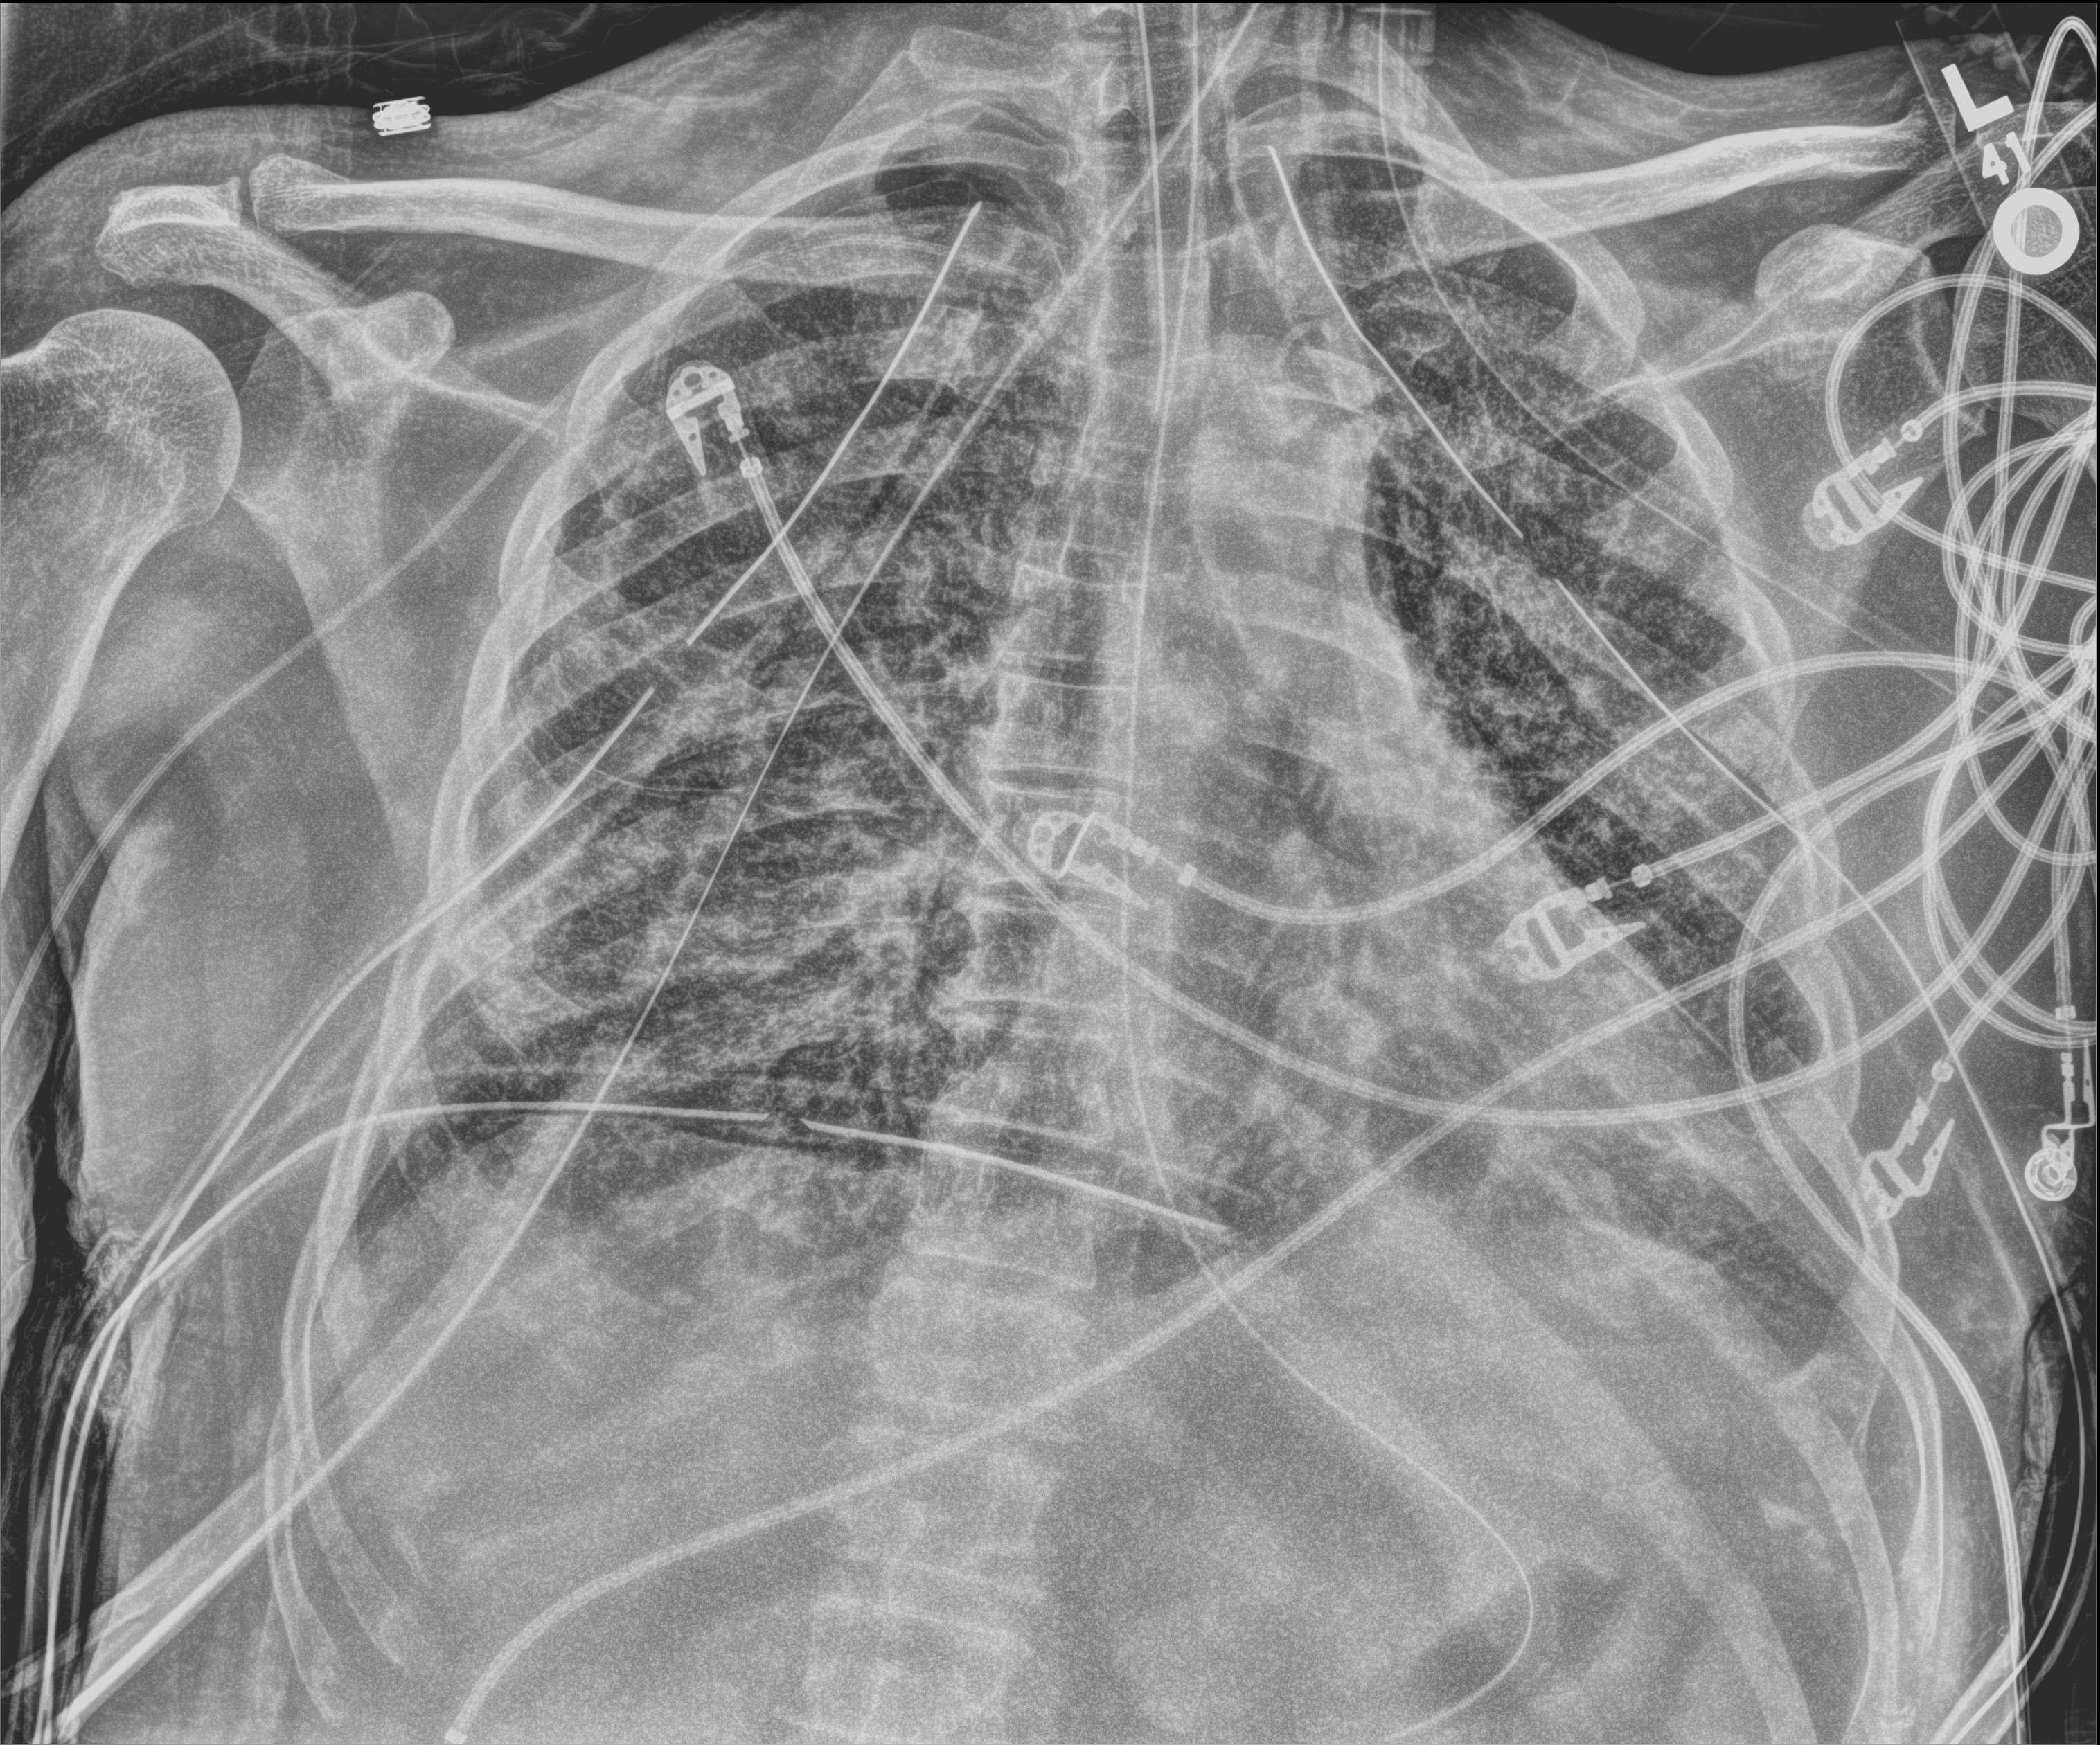
Chest X-ray (portable); anteroposterior (AP) projection. Patient hospitalised with COVID-19; male, aged 18–59 years.
Hospital-stay facts (about this admission, not read from this image; timing relative to this image not recorded): mechanically ventilated during this hospital stay: yes; hypertension (admission record): yes.